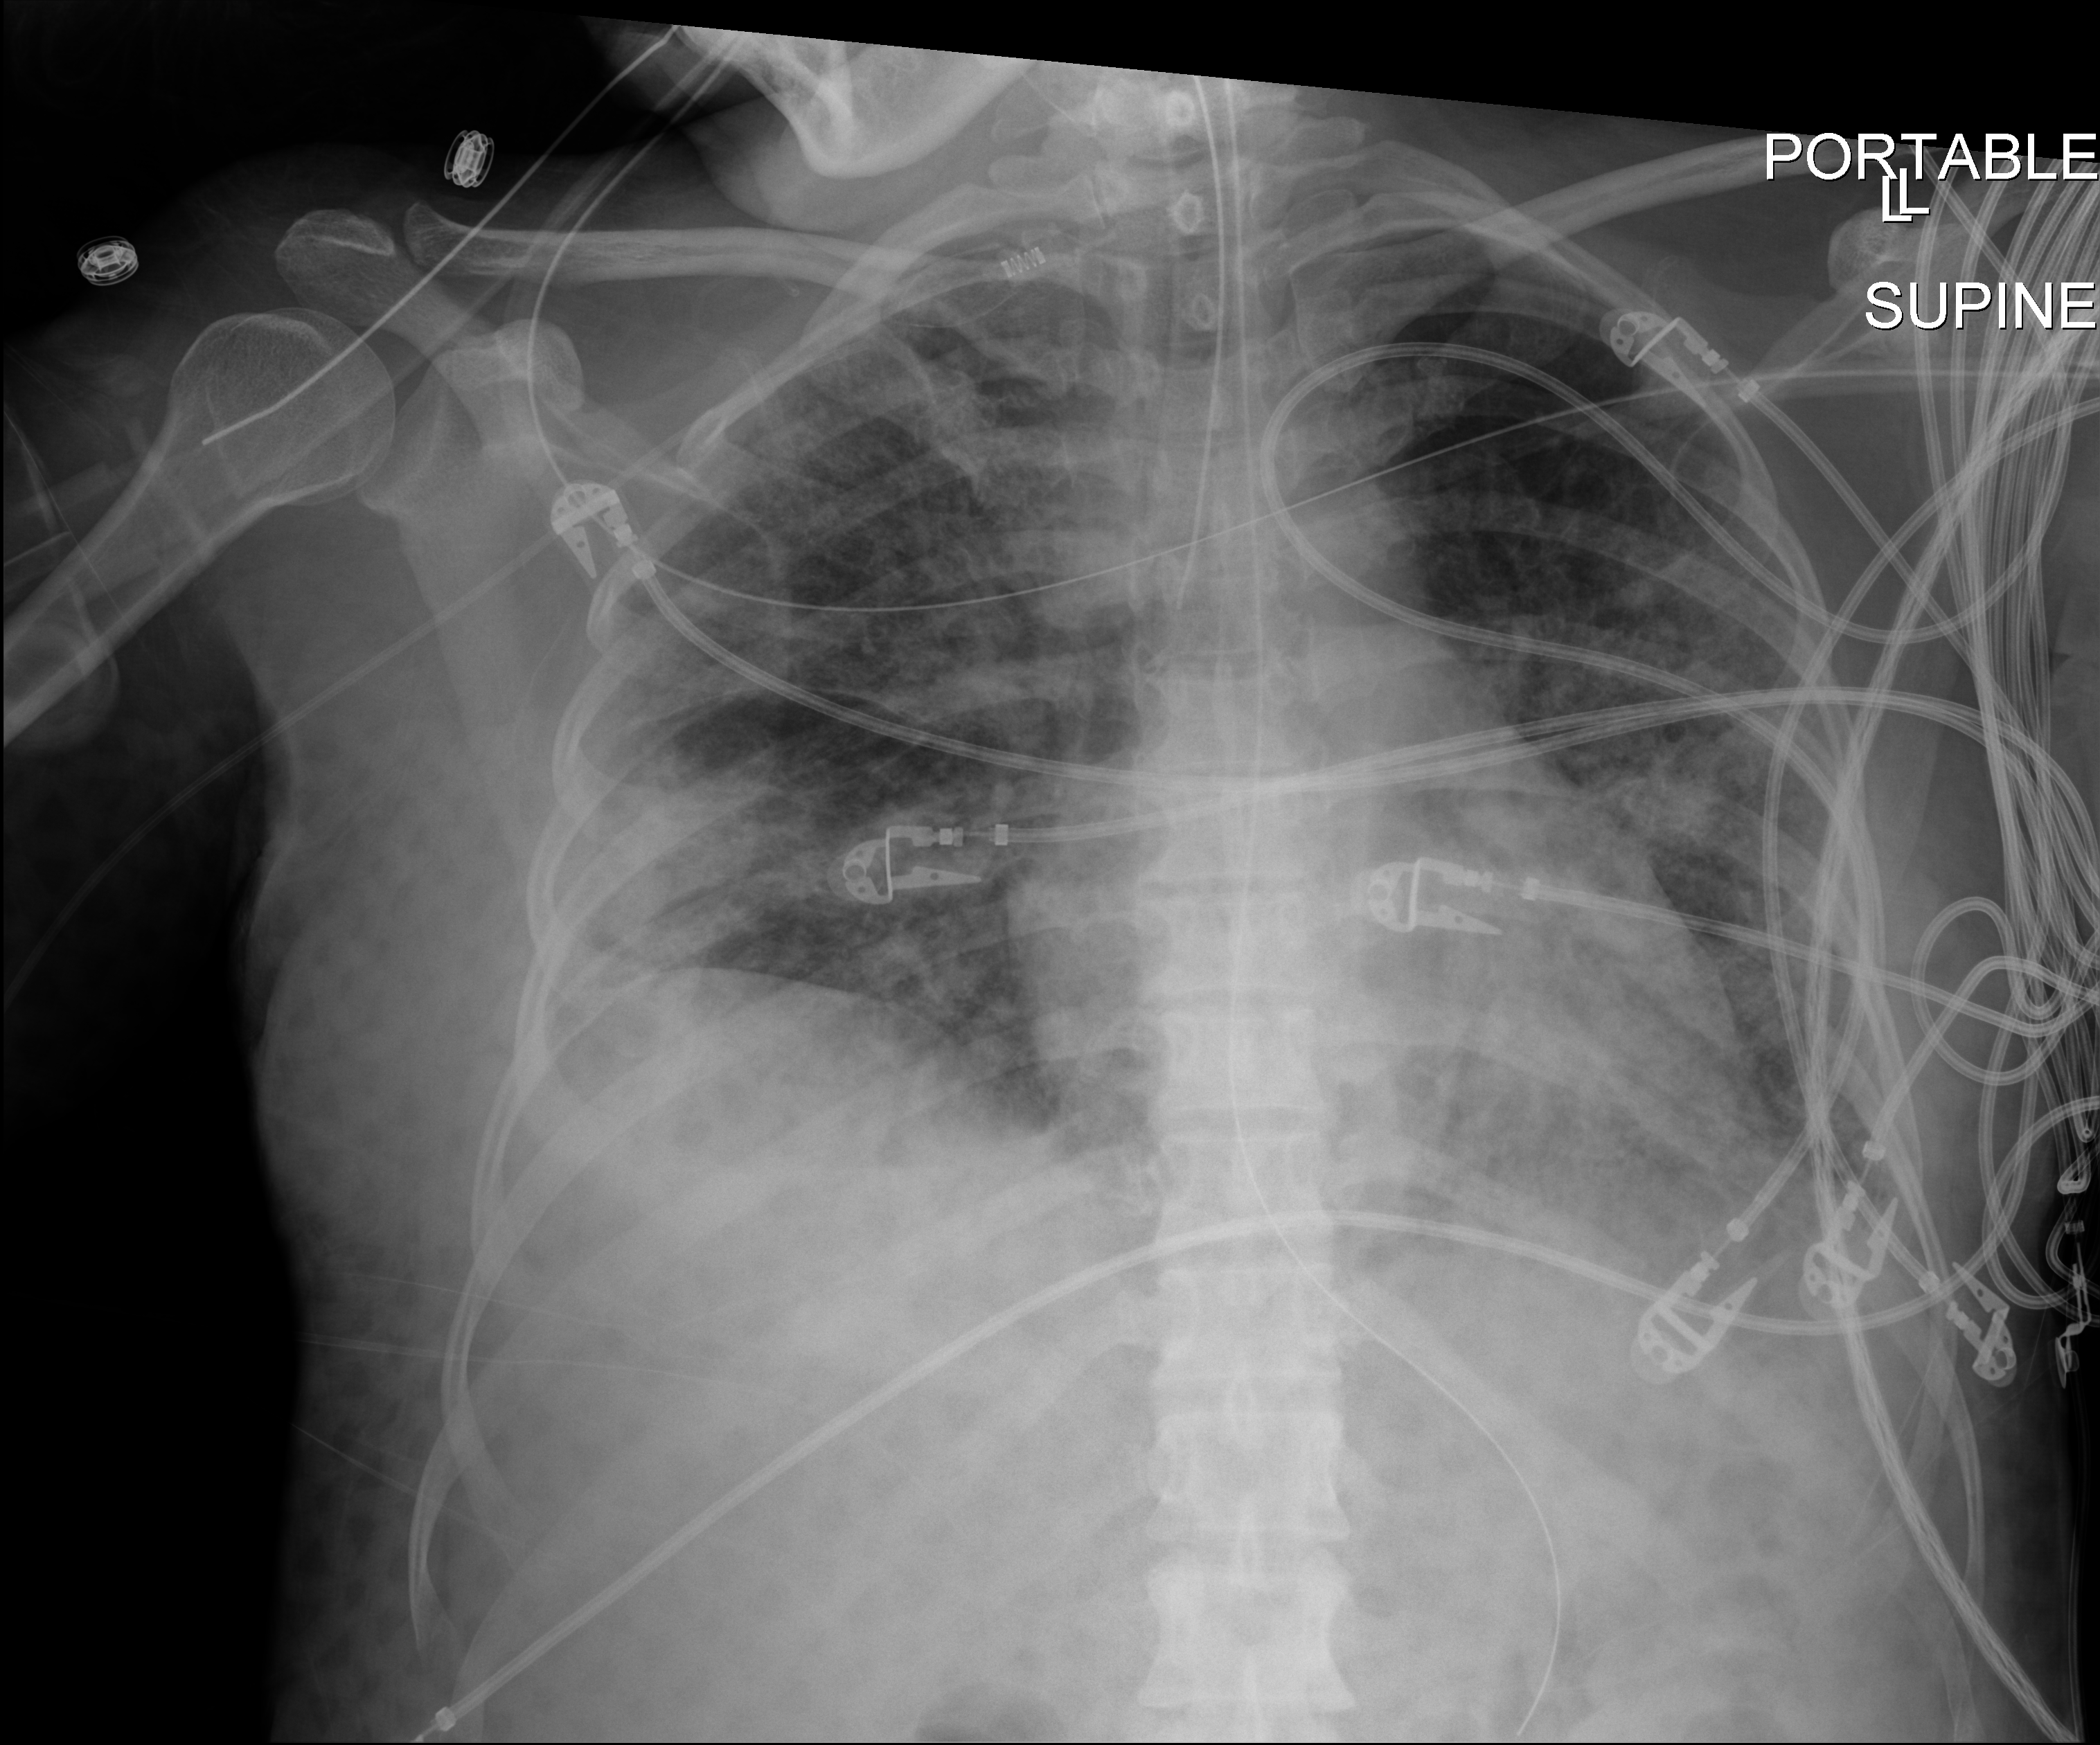
Chest X-ray (portable), anteroposterior (AP) projection. Female patient hospitalised with COVID-19, age 18–59 years.
From the hospital-stay record, not from the radiograph (when in the stay this image was taken is not recorded): admitted to intensive care during this hospital stay: yes; mechanically ventilated during this hospital stay: yes.